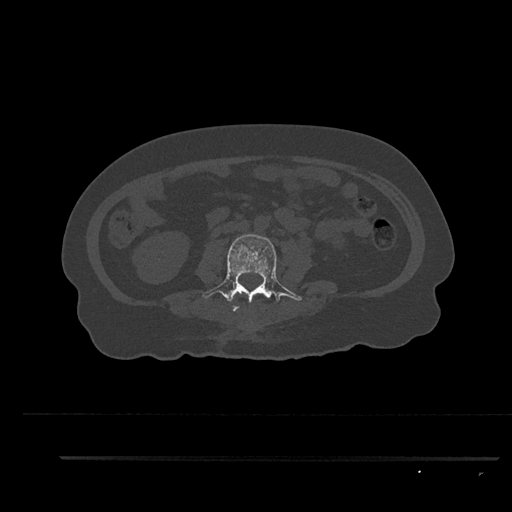
CT including the spine, one axial slice. Slice 94 of 797 in the series (ordered by position). Reconstruction kernel Br40s/3. Bone window (W 1800 / L 400 HU). 512 × 512 image matrix, field of view 408 × 408 mm. Patient: female, 44 years. Case-level facts recorded for this patient, not image findings: primary cancer: renal; vertebrae with lytic lesions (as recorded): L1.
Structures marked on this image (semi-automatic segmentation, software-assisted and operator-edited):
- L2 vertebra: box from (x=232, y=299) to (x=240, y=311) px
- L3 vertebra: (x=202, y=234)–(x=302, y=310)